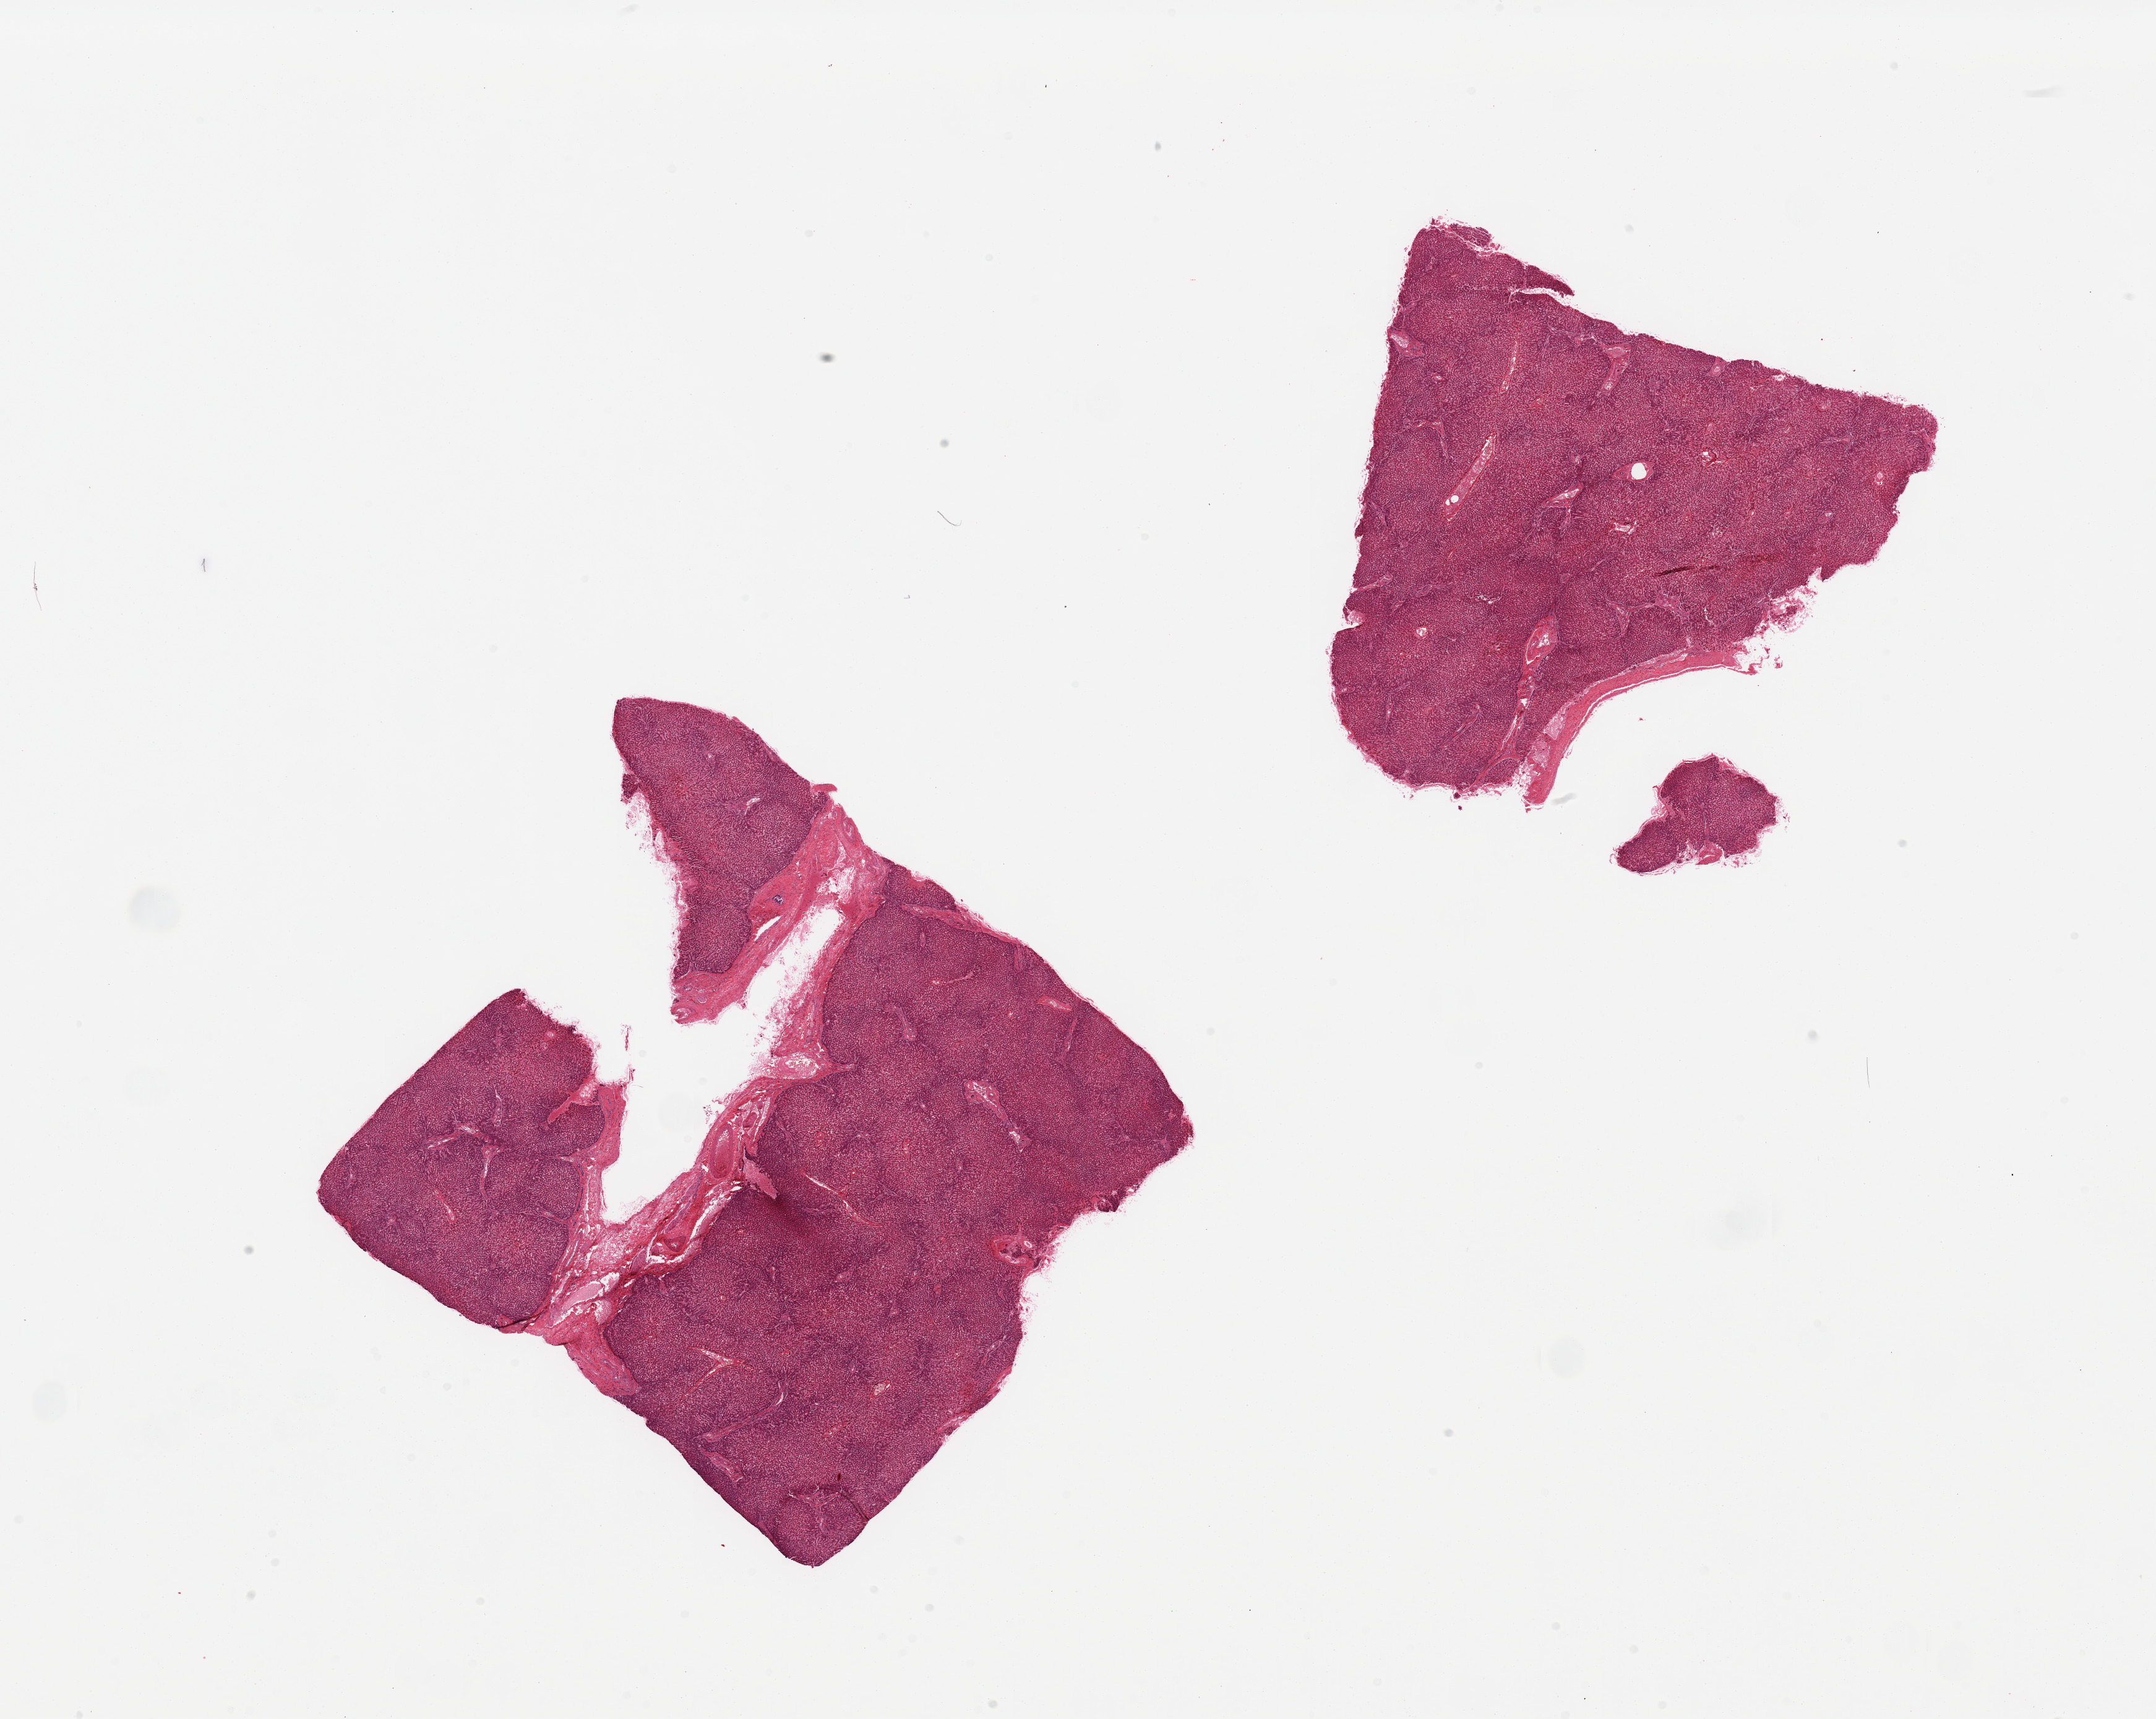
Haematoxylin and eosin whole-slide image, brightfield, a low-resolution overview of the entire scanned area, about 27.6 x 22.0 mm (slide scanned at 20x), PAXgene-fixed paraffin-embedded (PFPE) section, section of liver (target tissue), tissue donor sample. Male donor.
Review note (as recorded): 2 pieces moderate passive congestion.